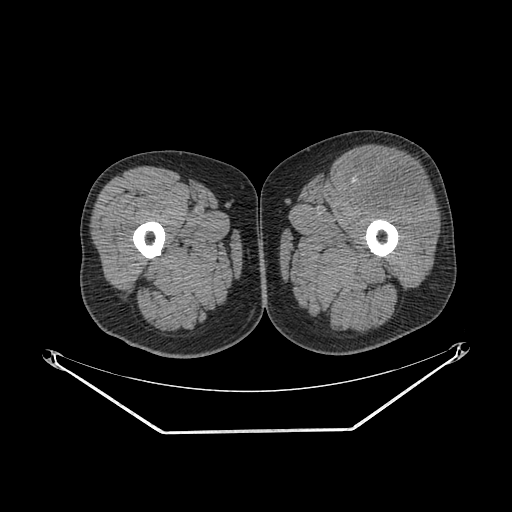
CT of an extremity soft-tissue mass (from a PET/CT study), one axial slice; position 238 of 267 along the scan axis; soft-tissue window (W 400 / L 40 HU); 3.75 mm slice thickness; 512 × 512 image matrix, field of view 500 × 500 mm. Male patient. From the clinical record (not read from this slice): histological type: extraskeletal osteosarcoma; grade: high; site of the primary tumour: thigh.
Outlined on this slice (expert contour drawn on MRI and transferred to this co-registered scan by the dataset authors):
- gross tumour volume (mass): bounding box (x1, y1, x2, y2) in pixels: (352, 158, 433, 211)